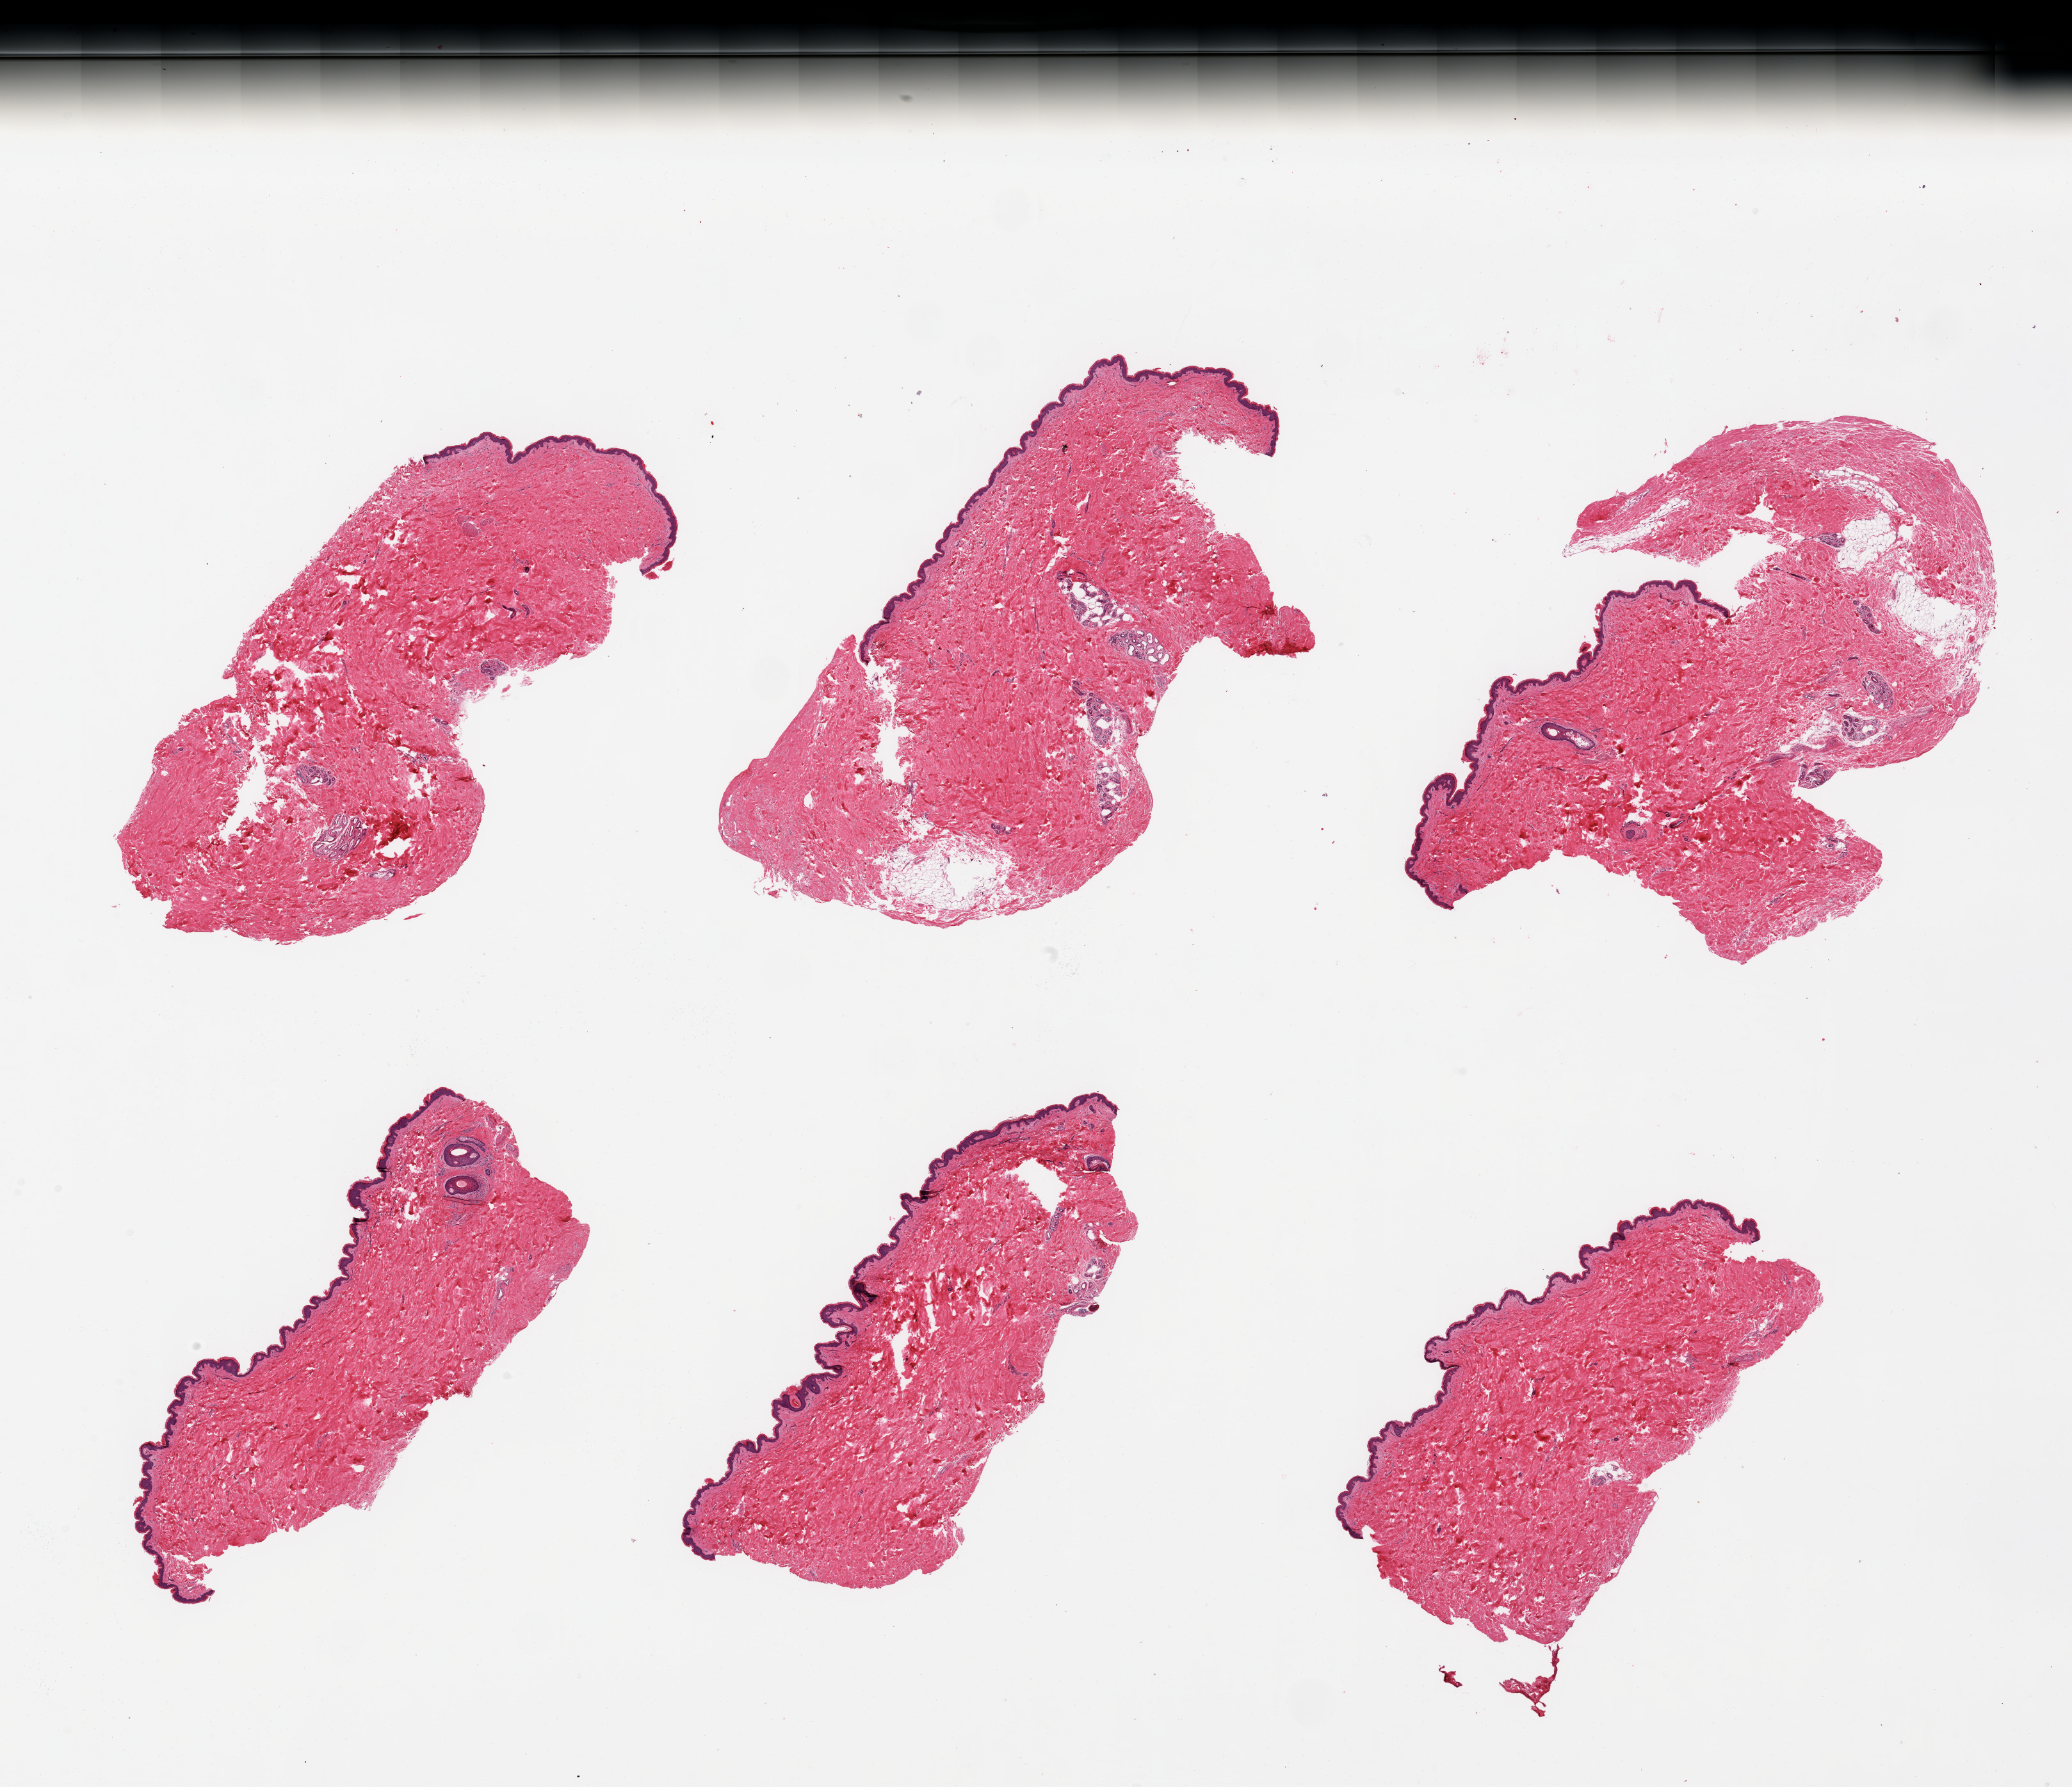
Hematoxylin and eosin (H&E) whole-slide image, shown as a low-resolution overview of the whole scanned area (about 25.6 x 22.1 mm). PAXgene-fixed, paraffin-embedded tissue. Section of skin of suprapubic region (target tissue). Tissue donor sample.
Pathologist's review note for this sample: 6 pieces; no dermal fat; squamous epithelium is ~45 microns.